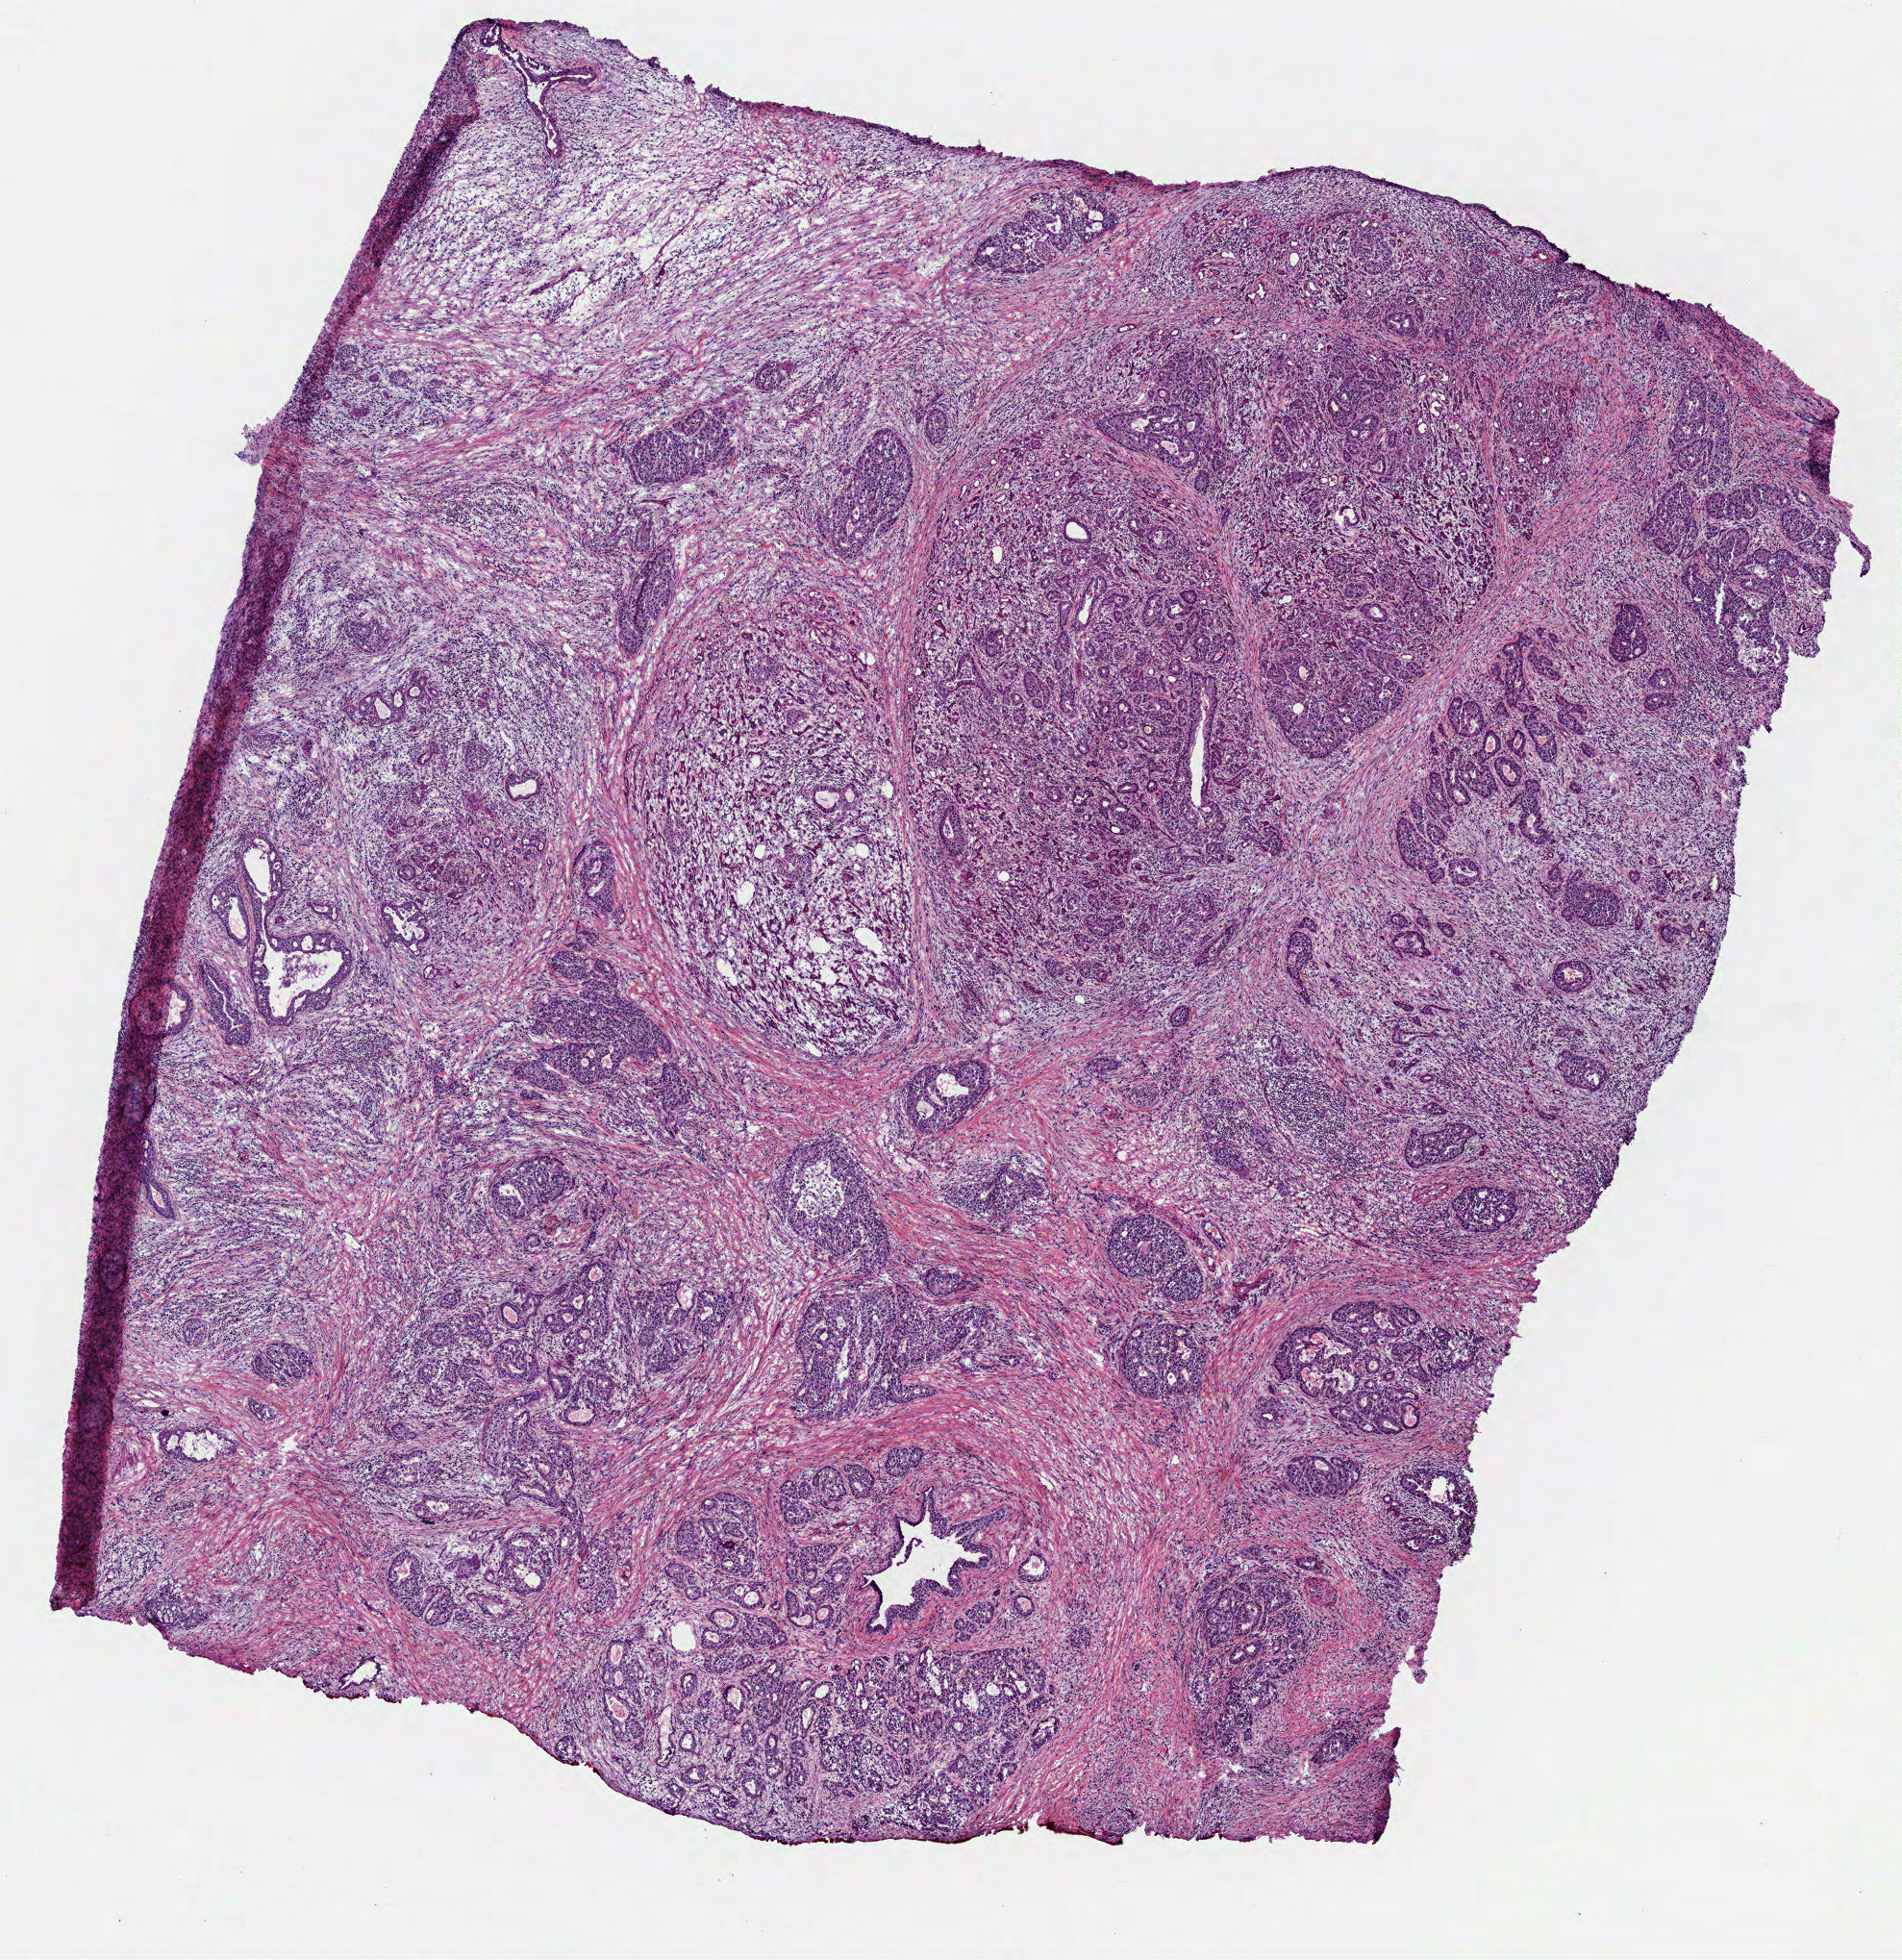
Whole-slide histology image, H&E, a low-resolution overview of the entire scanned area, about 8.0 x 8.2 mm (acquisition: 40x scan), frozen section from the top of the tissue portion, pancreas, primary tumour sample. Male patient; age at initial diagnosis 72 years. Histologic grade: G3 (poorly differentiated). Pathologist review of this section (percent, as recorded): tumour cells 90%, tumour nuclei 71%, normal cells 0%, stromal cells 10%, necrosis 0%. Inflammatory infiltration, as recorded: lymphocyte infiltration 15%, neutrophil infiltration 5%.
- AJCC pathologic stage: IIB (7th edition)
- lymph nodes positive (case pathology): 11 of 22 examined
- diagnosis: Infiltrating duct carcinoma, NOS (head of pancreas)